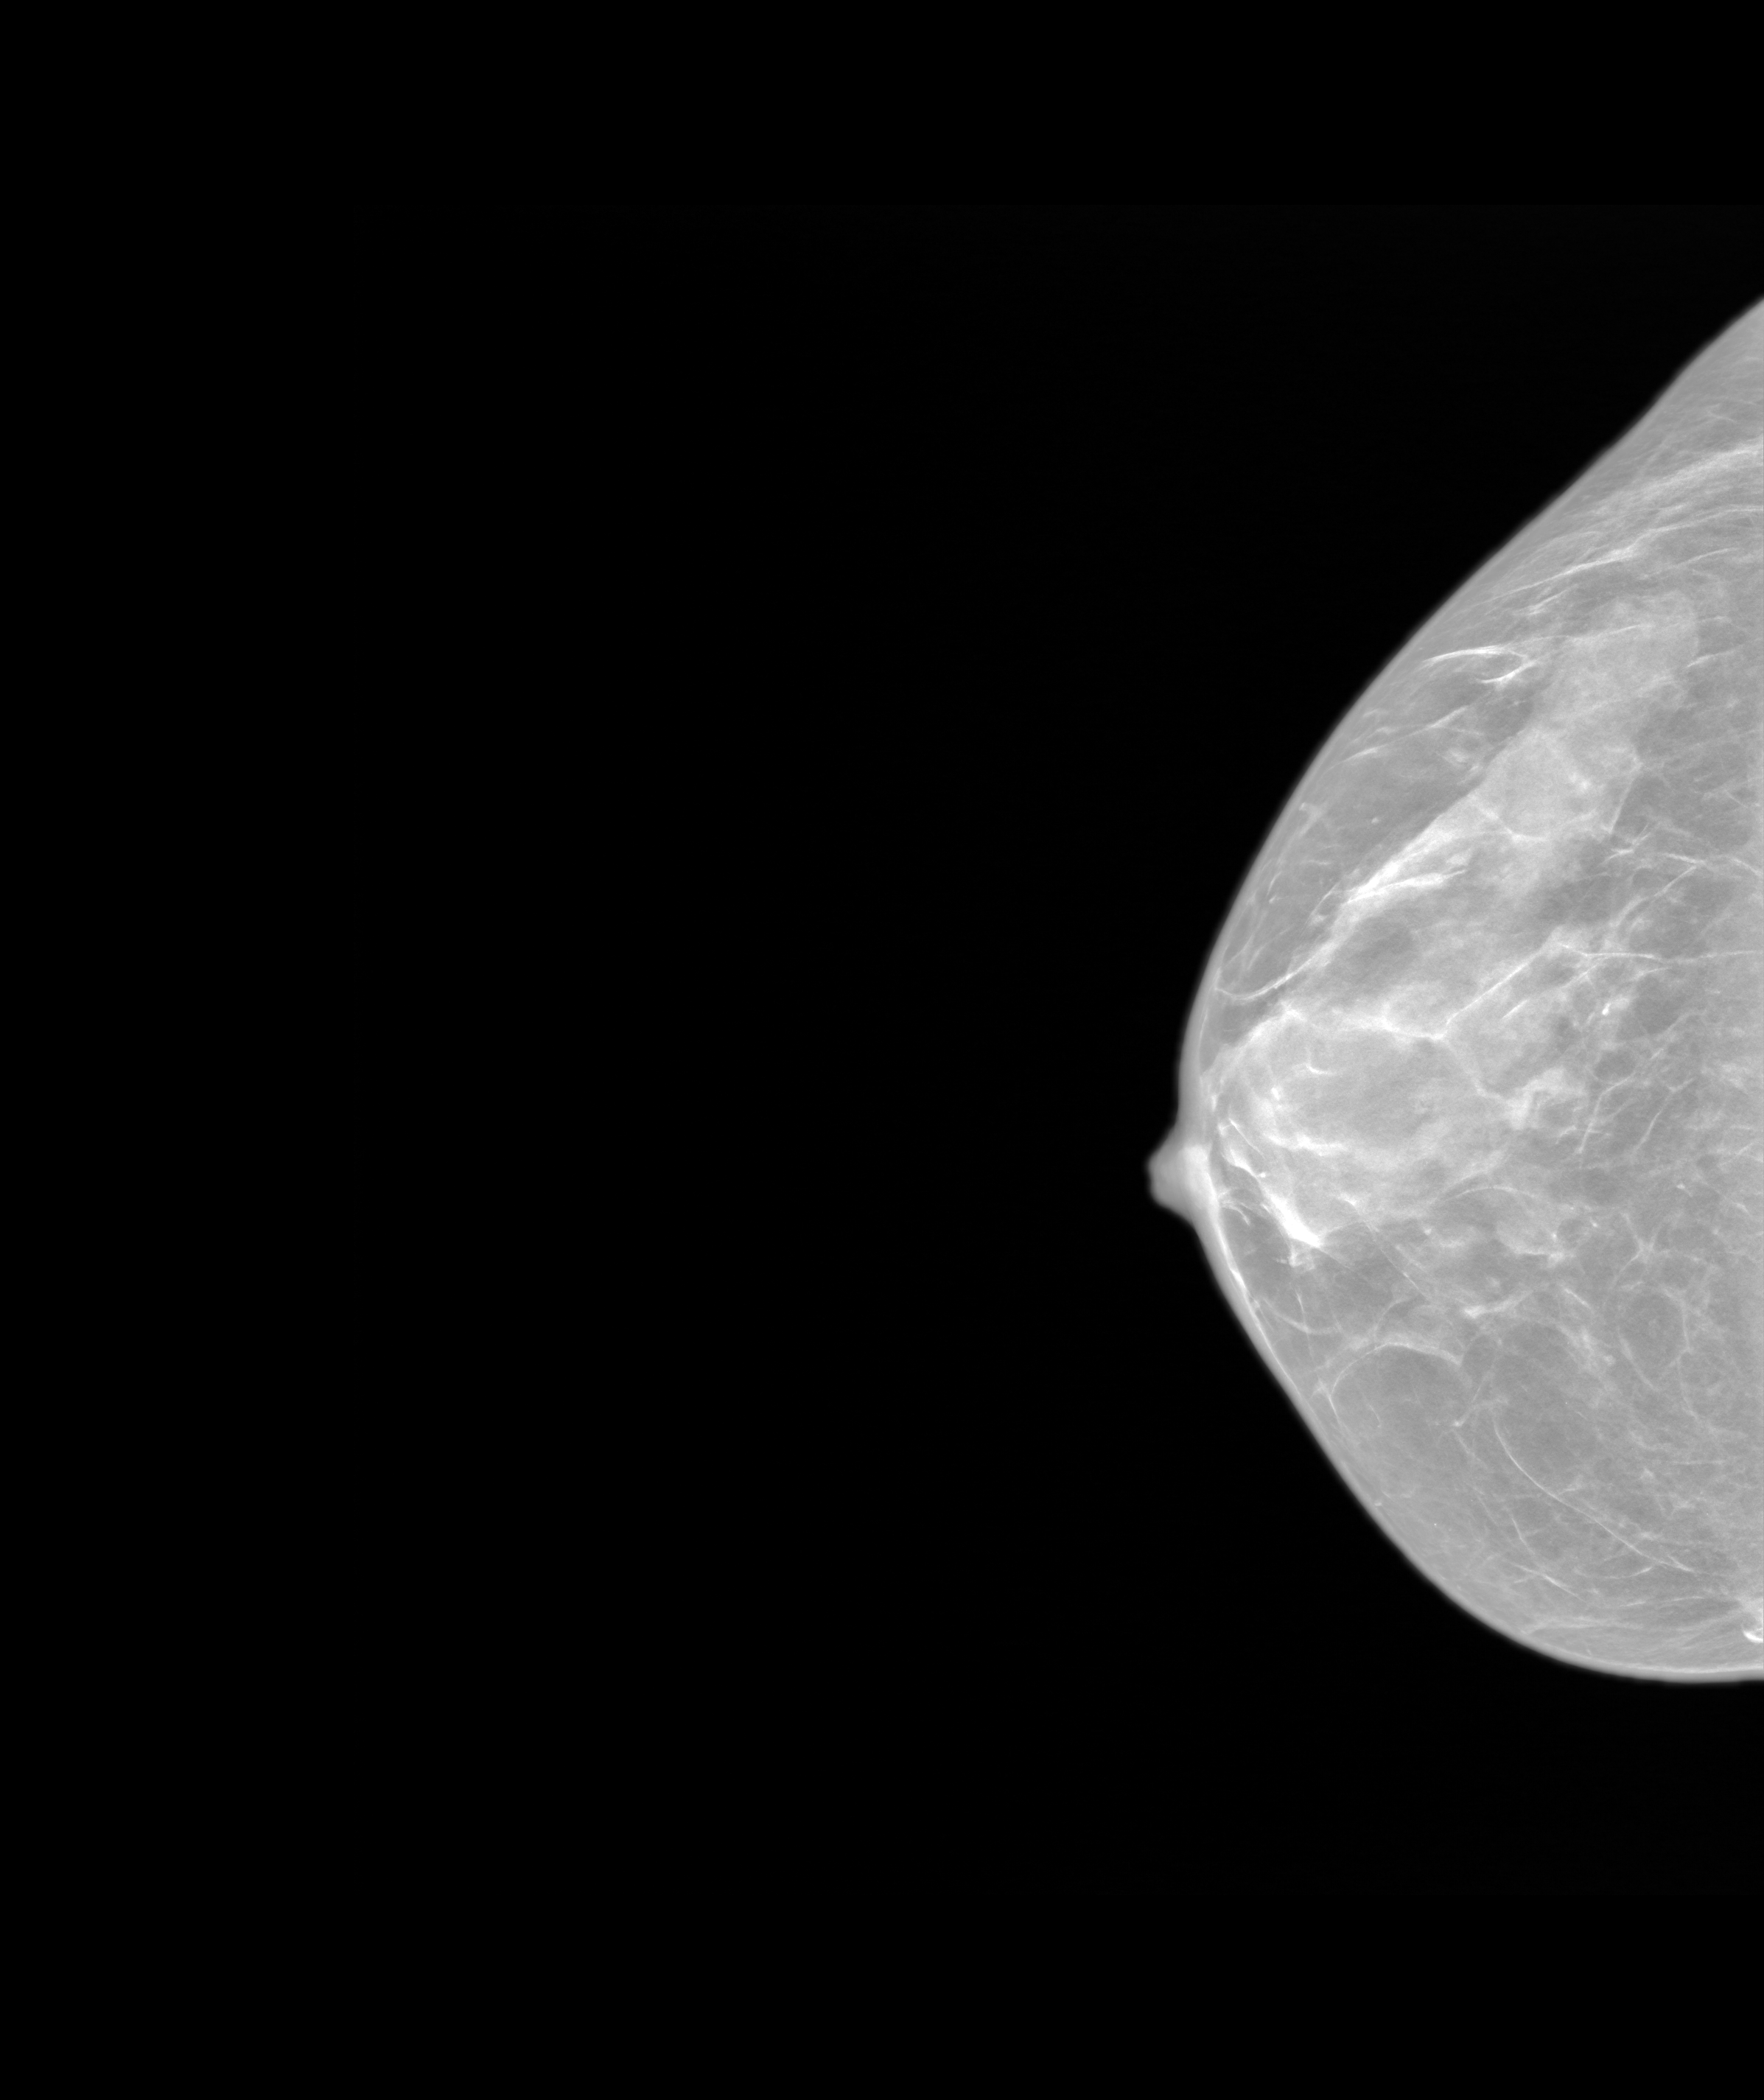
Synthetic 2-D view generated from a tomosynthesis acquisition (not an FFDM exposure); right breast; CC view; annual screening mammography examination. Patient aged 48 years (female).
- BI-RADS breast density category at the screening exam (both breasts, scale 1–4): 3
- final BI-RADS category for the screening round (tomosynthesis exam, both breasts): category 2
- recall: no recall after this screen